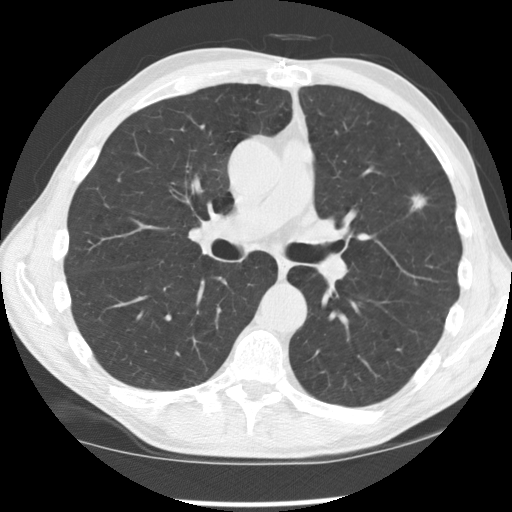
Low-dose screening chest CT, one axial slice. Position 99 of 170 along the scan axis. Lung window (W 1500 / L -600 HU). 2.5 mm slice thickness. 512 × 512 image matrix.
Annotated regions visible in this slice (outlined manually by an expert reader):
- lesion 1 (tumor, upper lobe of left lung): bounding box <411,194,426,211> (left, top, right, bottom; pixels)